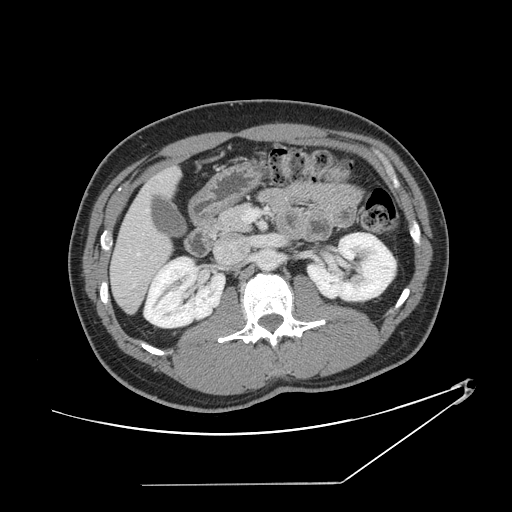
Contrast-enhanced abdominal CT, one axial slice; slice 62 of 152 in the series (ordered by position); 120 kVp; intravenous contrast given; soft-tissue window (W 400 / L 40 HU); 512 × 512 image matrix, field of view 432 × 432 mm. Male patient, age 45 years. From the clinical record (not read from this slice): diagnosis: colorectal cancer liver metastases, imaged before liver resection; multiple liver metastases: no; largest metastasis: 1 cm; disease in both lobes: no.
Annotated regions visible in this slice (outlined manually by an expert reader):
- hepatic veins: bounding box <136,210,148,257> (left, top, right, bottom; pixels)
- liver: <111,170,178,312>
- planned liver remnant (the part of the liver to remain after resection): <111,170,178,312>
- portal vein (with intrahepatic branches): <243,210,258,221>